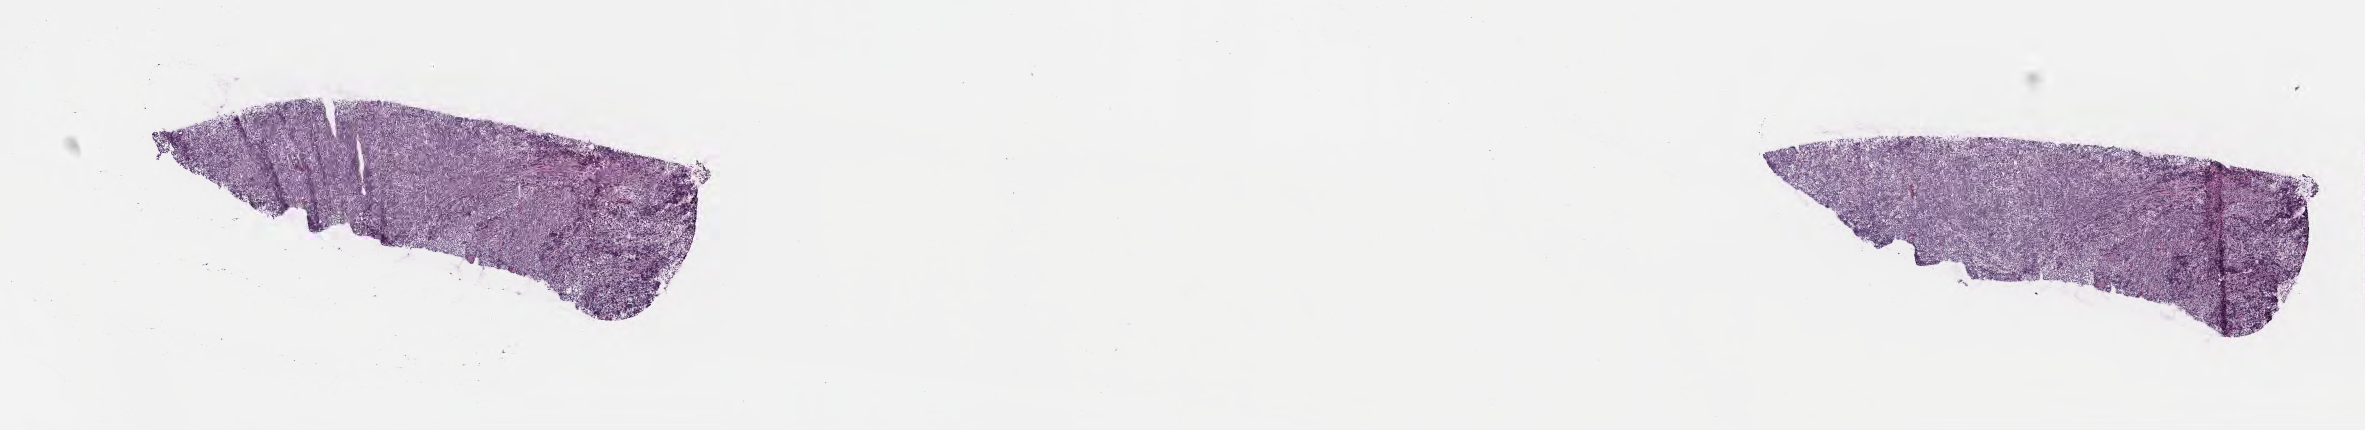
Digitized haematoxylin and eosin-stained section — shown as a low-resolution overview of the whole scanned area (about 19.1 x 3.5 mm). Cryosection. Primary tumor. Site: lymph node of head and neck. Patient: female, aged 11. Pathologist review of this section (percent, as recorded): tumor cells 90%, tumor nuclei 90%, stromal cells 10%, necrosis 0%, normal cells 0%. Infiltration values recorded for this section: lymphocyte infiltration 40%, monocyte infiltration 3%, neutrophil infiltration 5%.
* histologic diagnosis: Burkitt lymphoma, NOS
* Ann Arbor stage (patient): Stage II